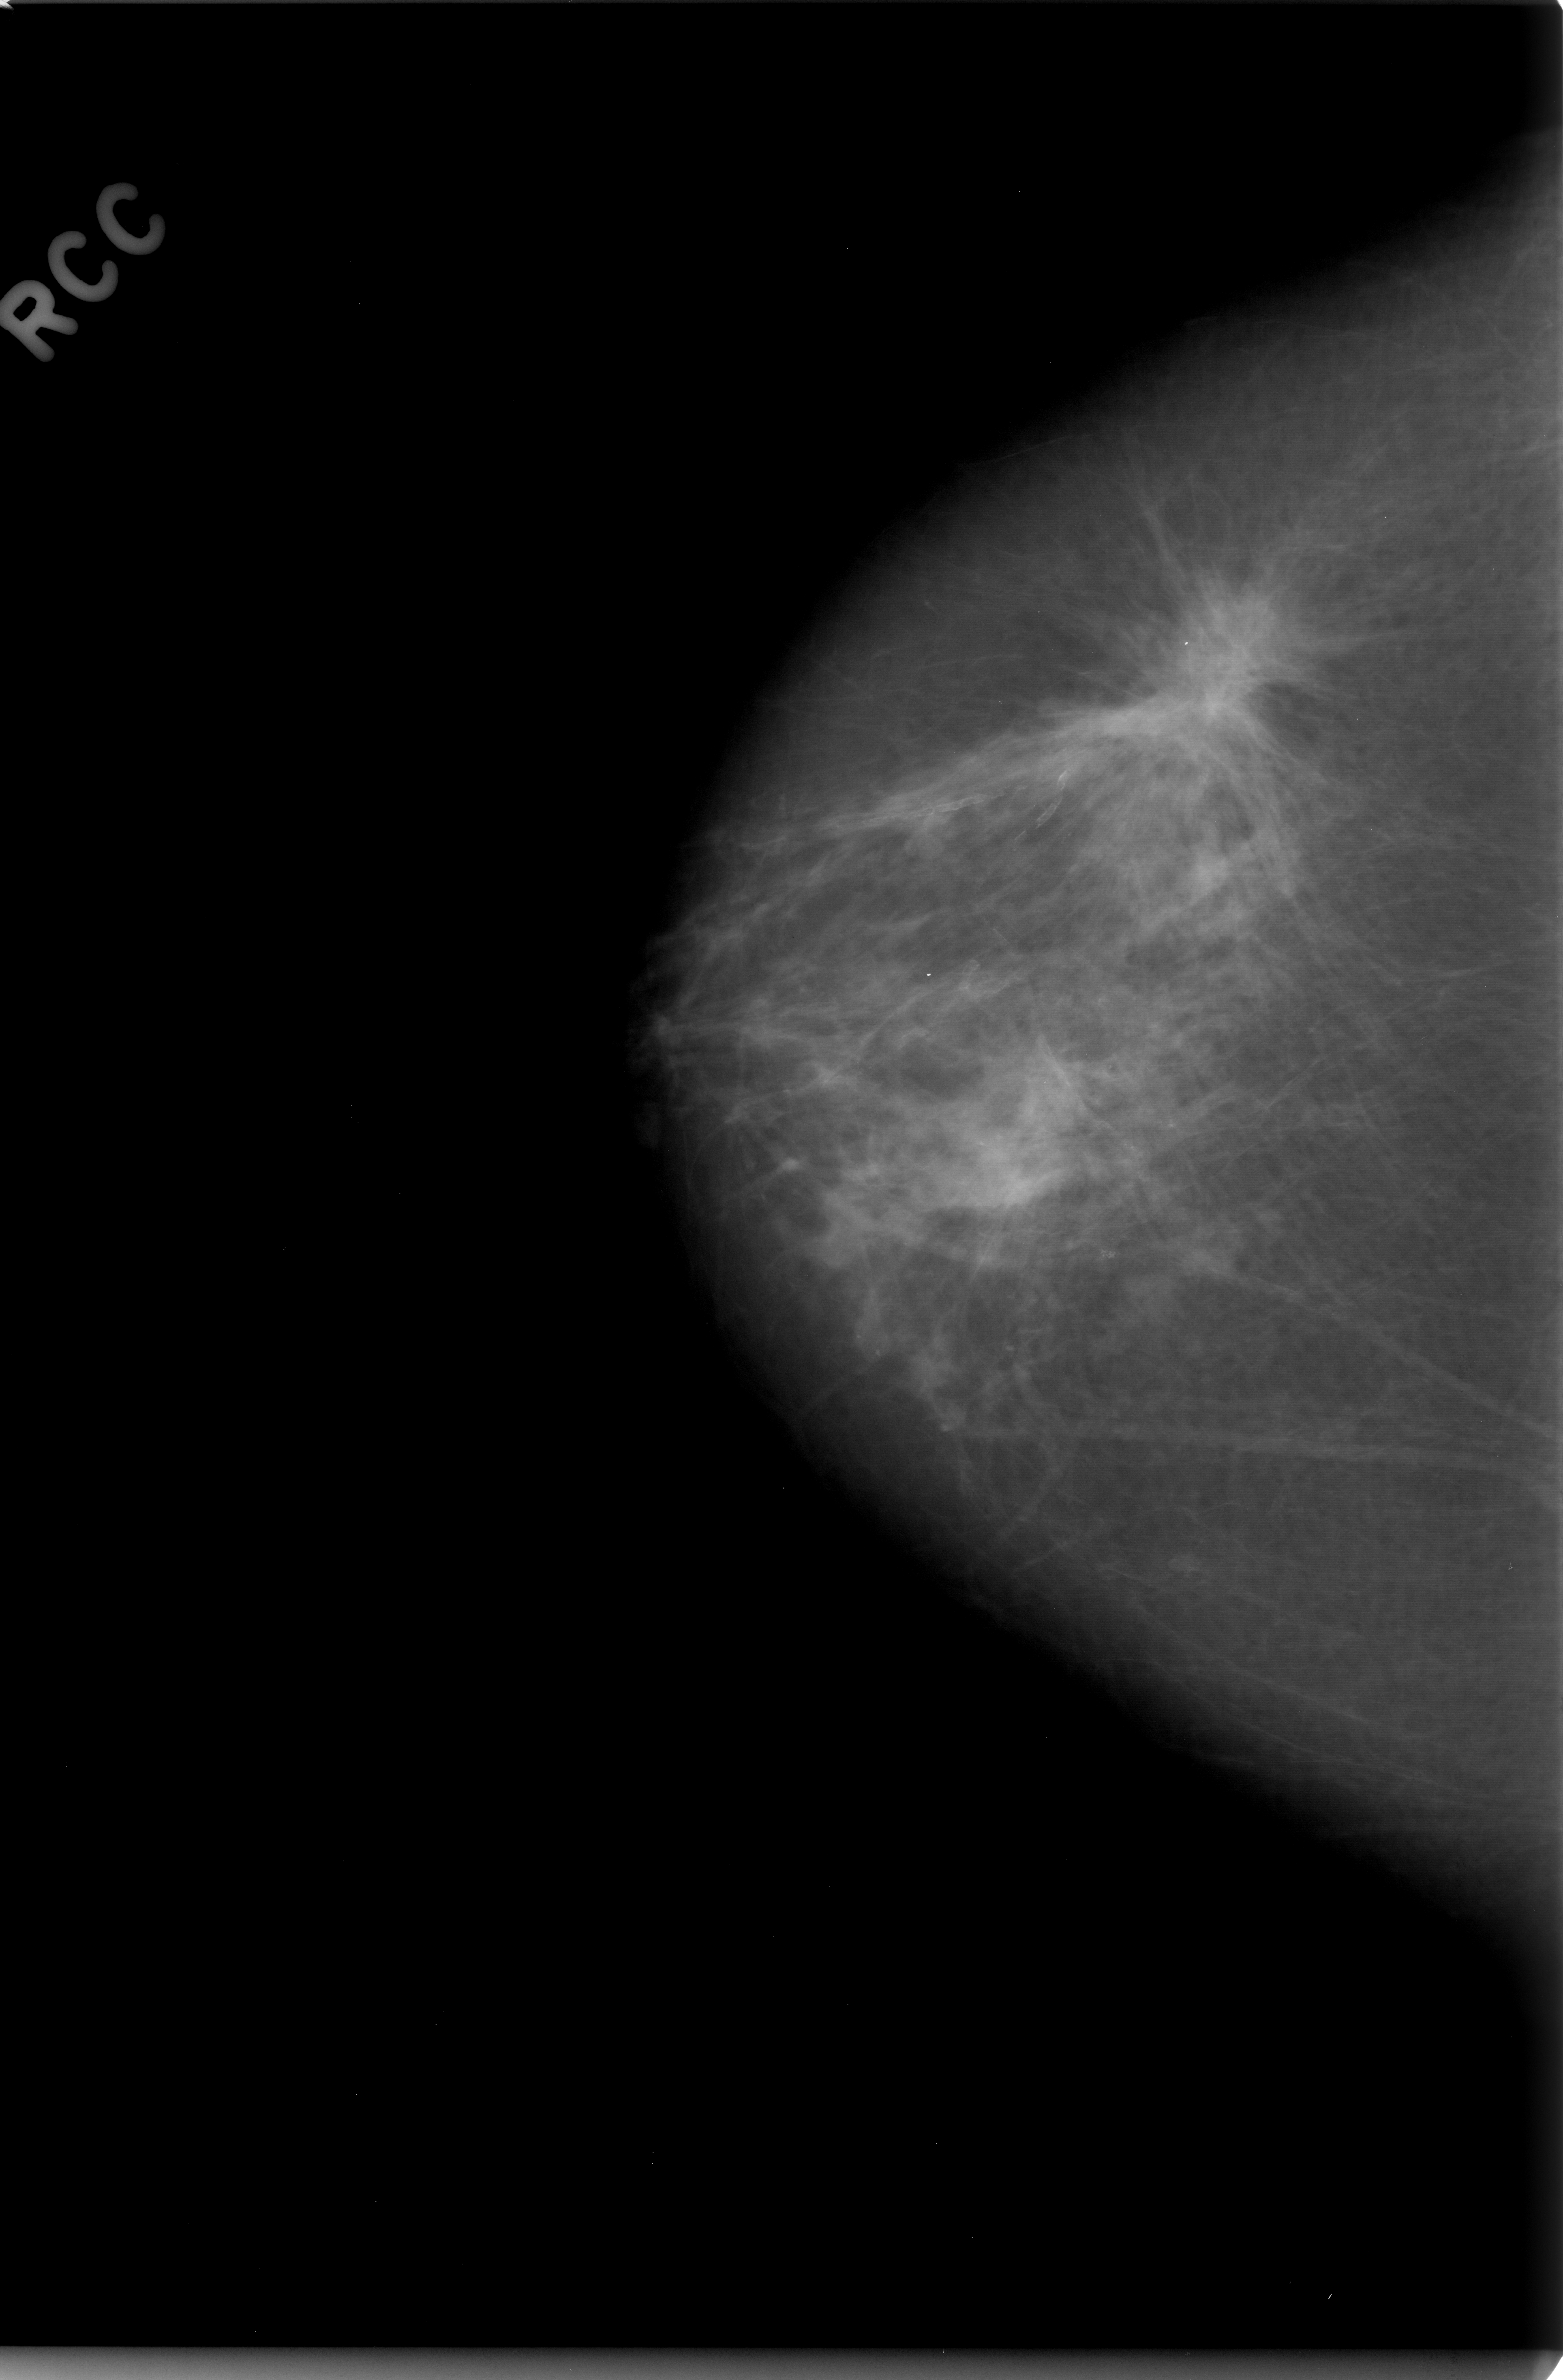
Digitized screen-film mammogram. Right breast. CC view. BI-RADS breast density category 2 (scale 1–4). 1563 × 2380 image matrix.
Expert-marked regions of interest on this film, with their recorded descriptors:
- mass, shape architectural distortion, margins spiculated; BI-RADS assessment category 2; subtlety rating 5 on a 1 (subtle) to 5 (obvious) scale; pathology result (as recorded, not read from the image): benign: bounding box (x1, y1, x2, y2) in pixels: (1091, 596, 1308, 806)